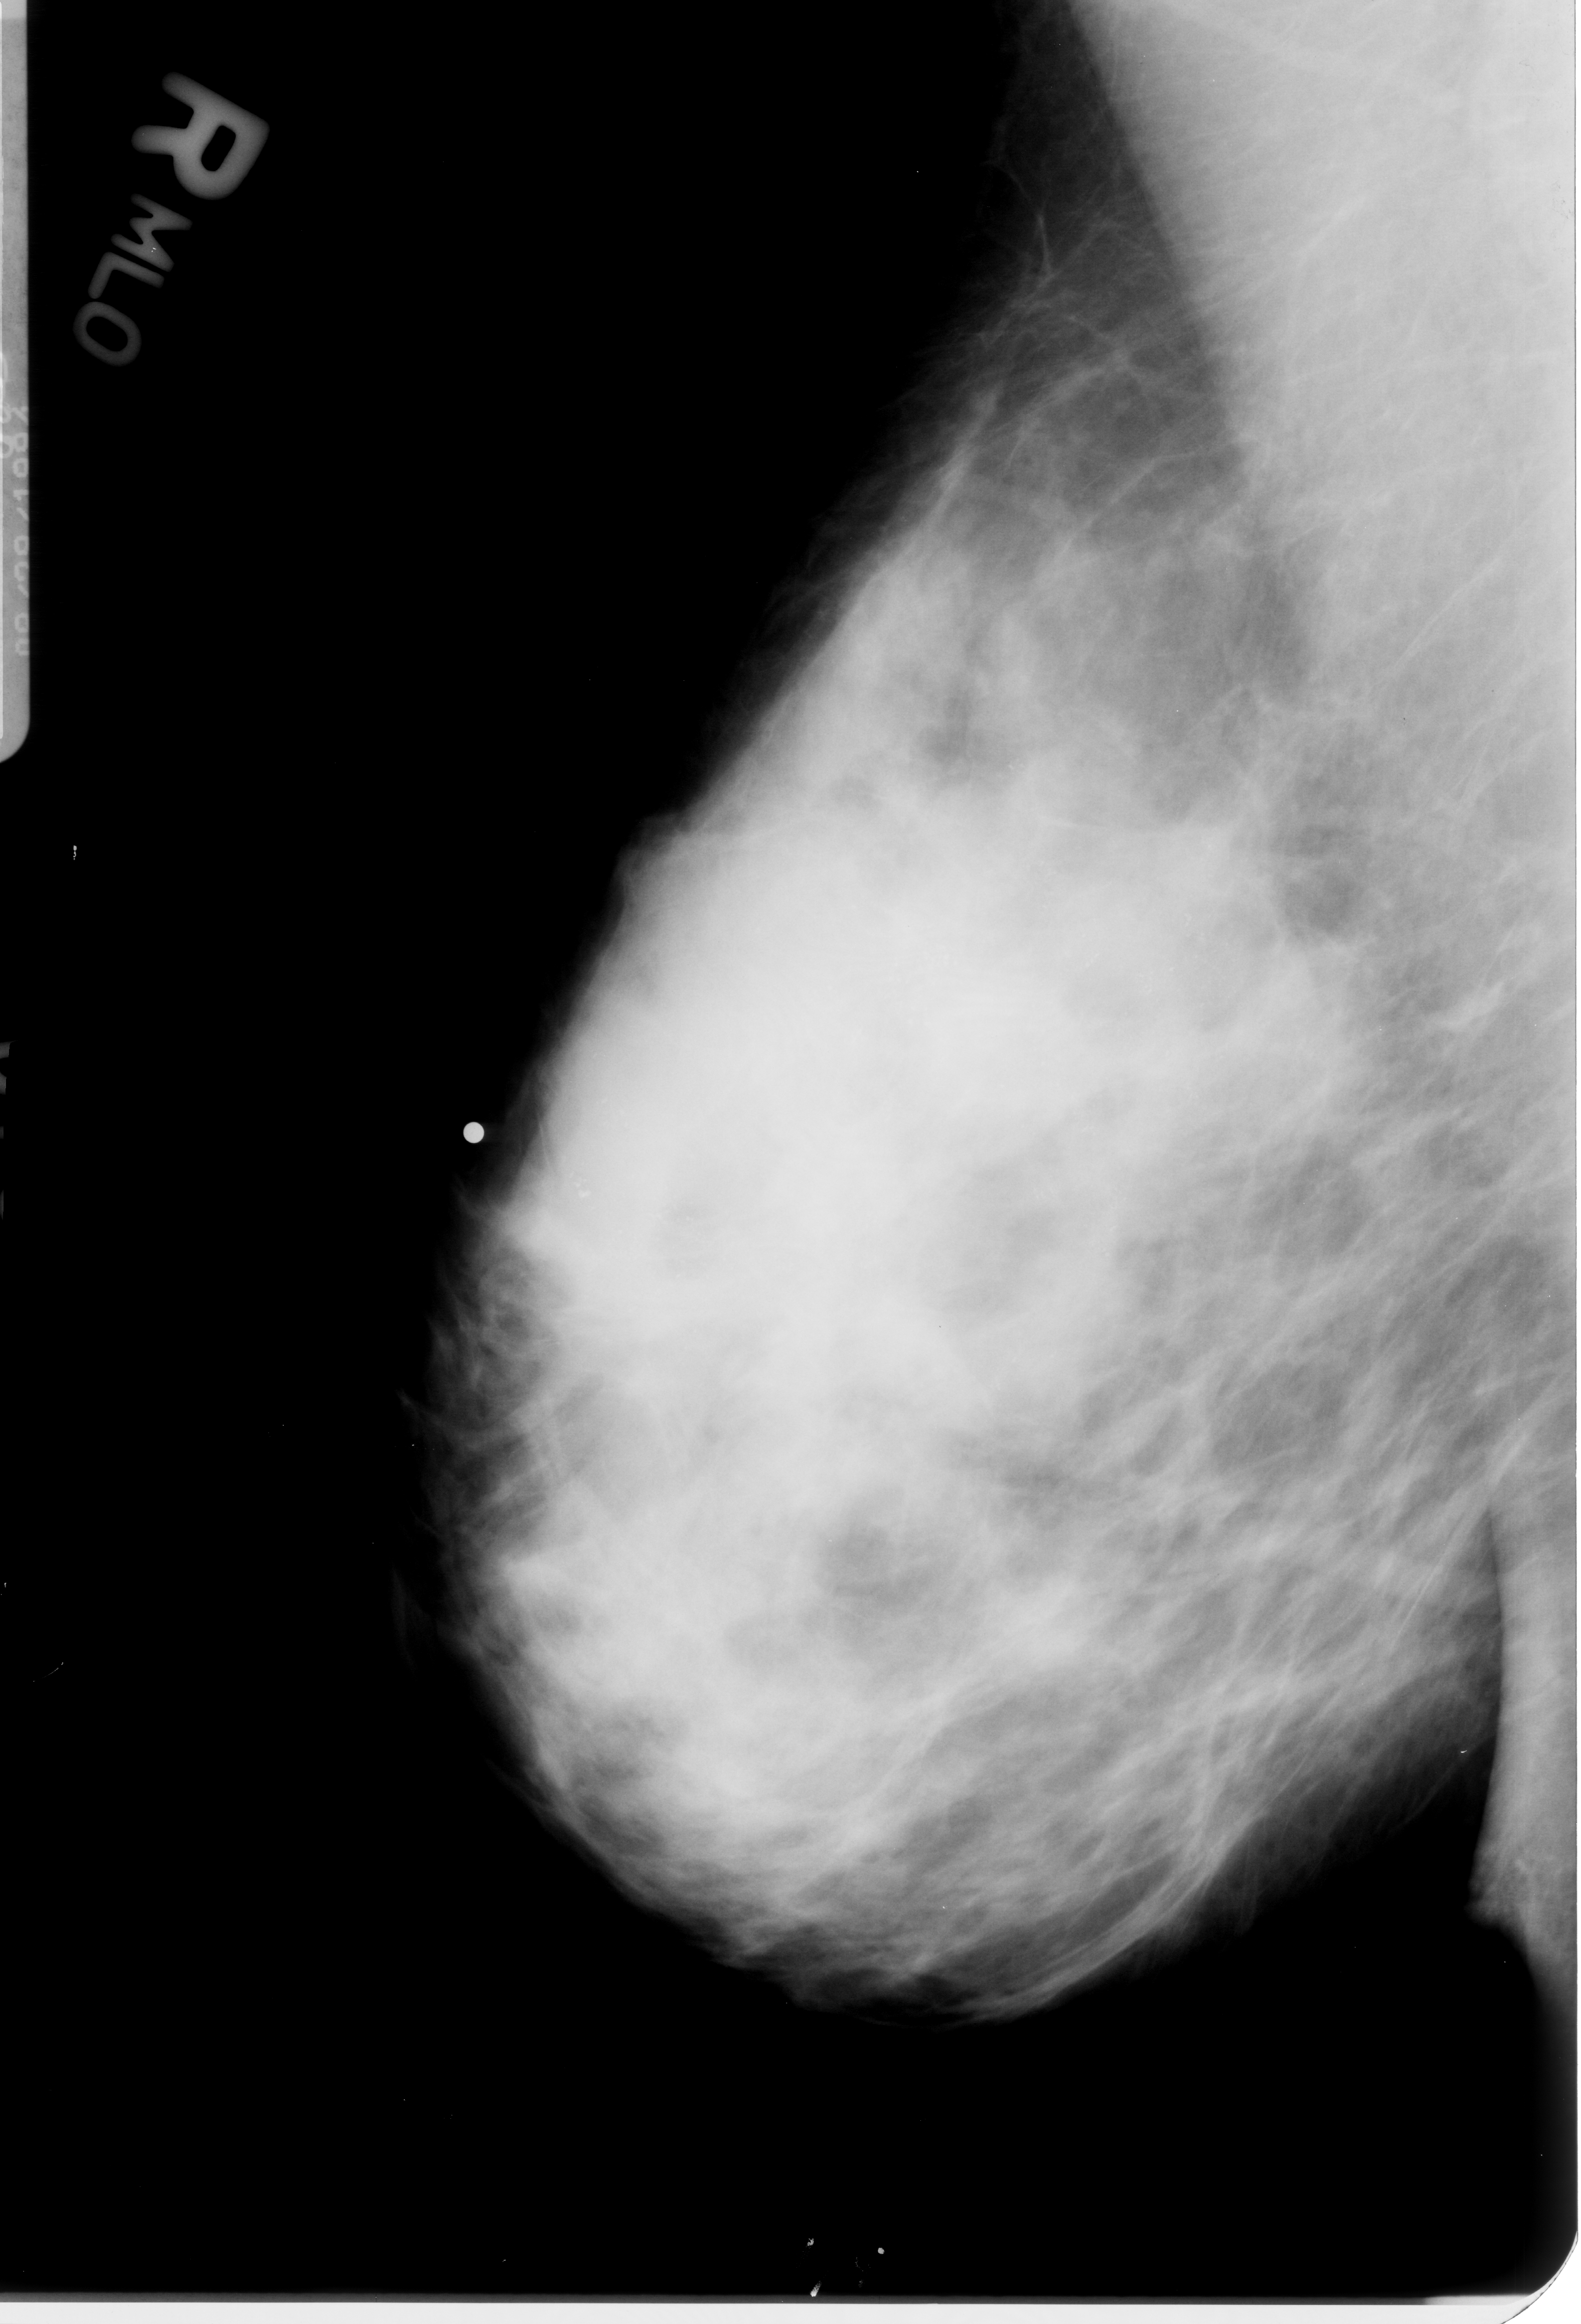
Mammogram (digitized film); right breast; mediolateral oblique (MLO) view; BI-RADS breast density category 3 (scale 1–4); 1581 × 2324 image matrix.
Expert-marked regions of interest on this image (one box per marked abnormality):
- calcifications, morphology pleomorphic, distribution regional; BI-RADS assessment category 5; subtlety rating 3 on a 1 (subtle) to 5 (obvious) scale; pathology (as recorded): malignant: bounding box [x1, y1, x2, y2] px = [497, 670, 1417, 1458]